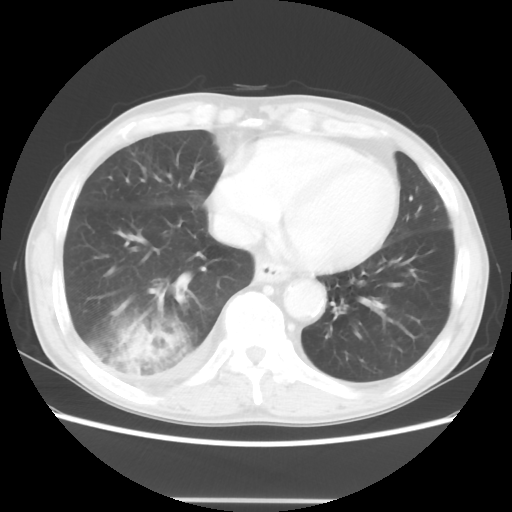
Chest CT, one axial slice. Position 12 of 48 along the scan axis. 100 kVp. Lung window (W 1500 / L -600 HU). 5 mm slice thickness. 512 × 512 image matrix, field of view 361 × 361 mm. Patient: male, 66 years. Case-level facts recorded for this patient, not image findings: clinical TNM (as recorded): T4 N1 M1; histopathological grade: G3.
Structures marked on this image (bounding box drawn by a radiologist):
- lung tumour (recorded histology: small cell carcinoma): bounding box [x1, y1, x2, y2] px = [107, 318, 192, 389]